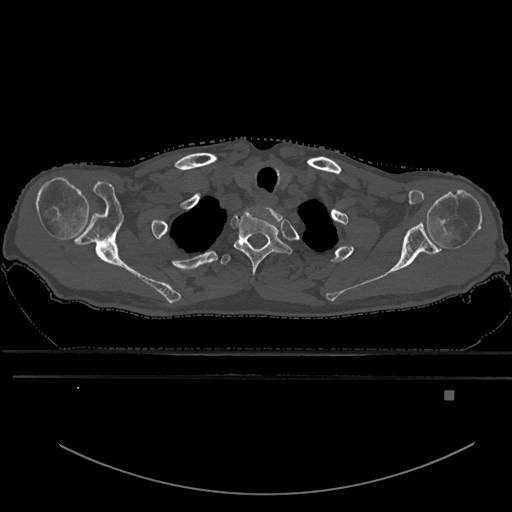
CT including the spine, one axial slice. Slice 535 of 969 in the series (ordered by position). Bone window (W 1800 / L 400 HU). 512 × 512 image matrix. Patient: male, 82 years. From the clinical record (not read from this slice): primary cancer: prostate; vertebrae with lytic lesions (as recorded): T11, T9, T8, T2.
Outlined on this slice (semi-automatic segmentation, software-assisted and operator-edited):
- T1 vertebra: bounding box [x1, y1, x2, y2] px = [233, 211, 291, 276]
- T2 vertebra: [220, 254, 232, 266]